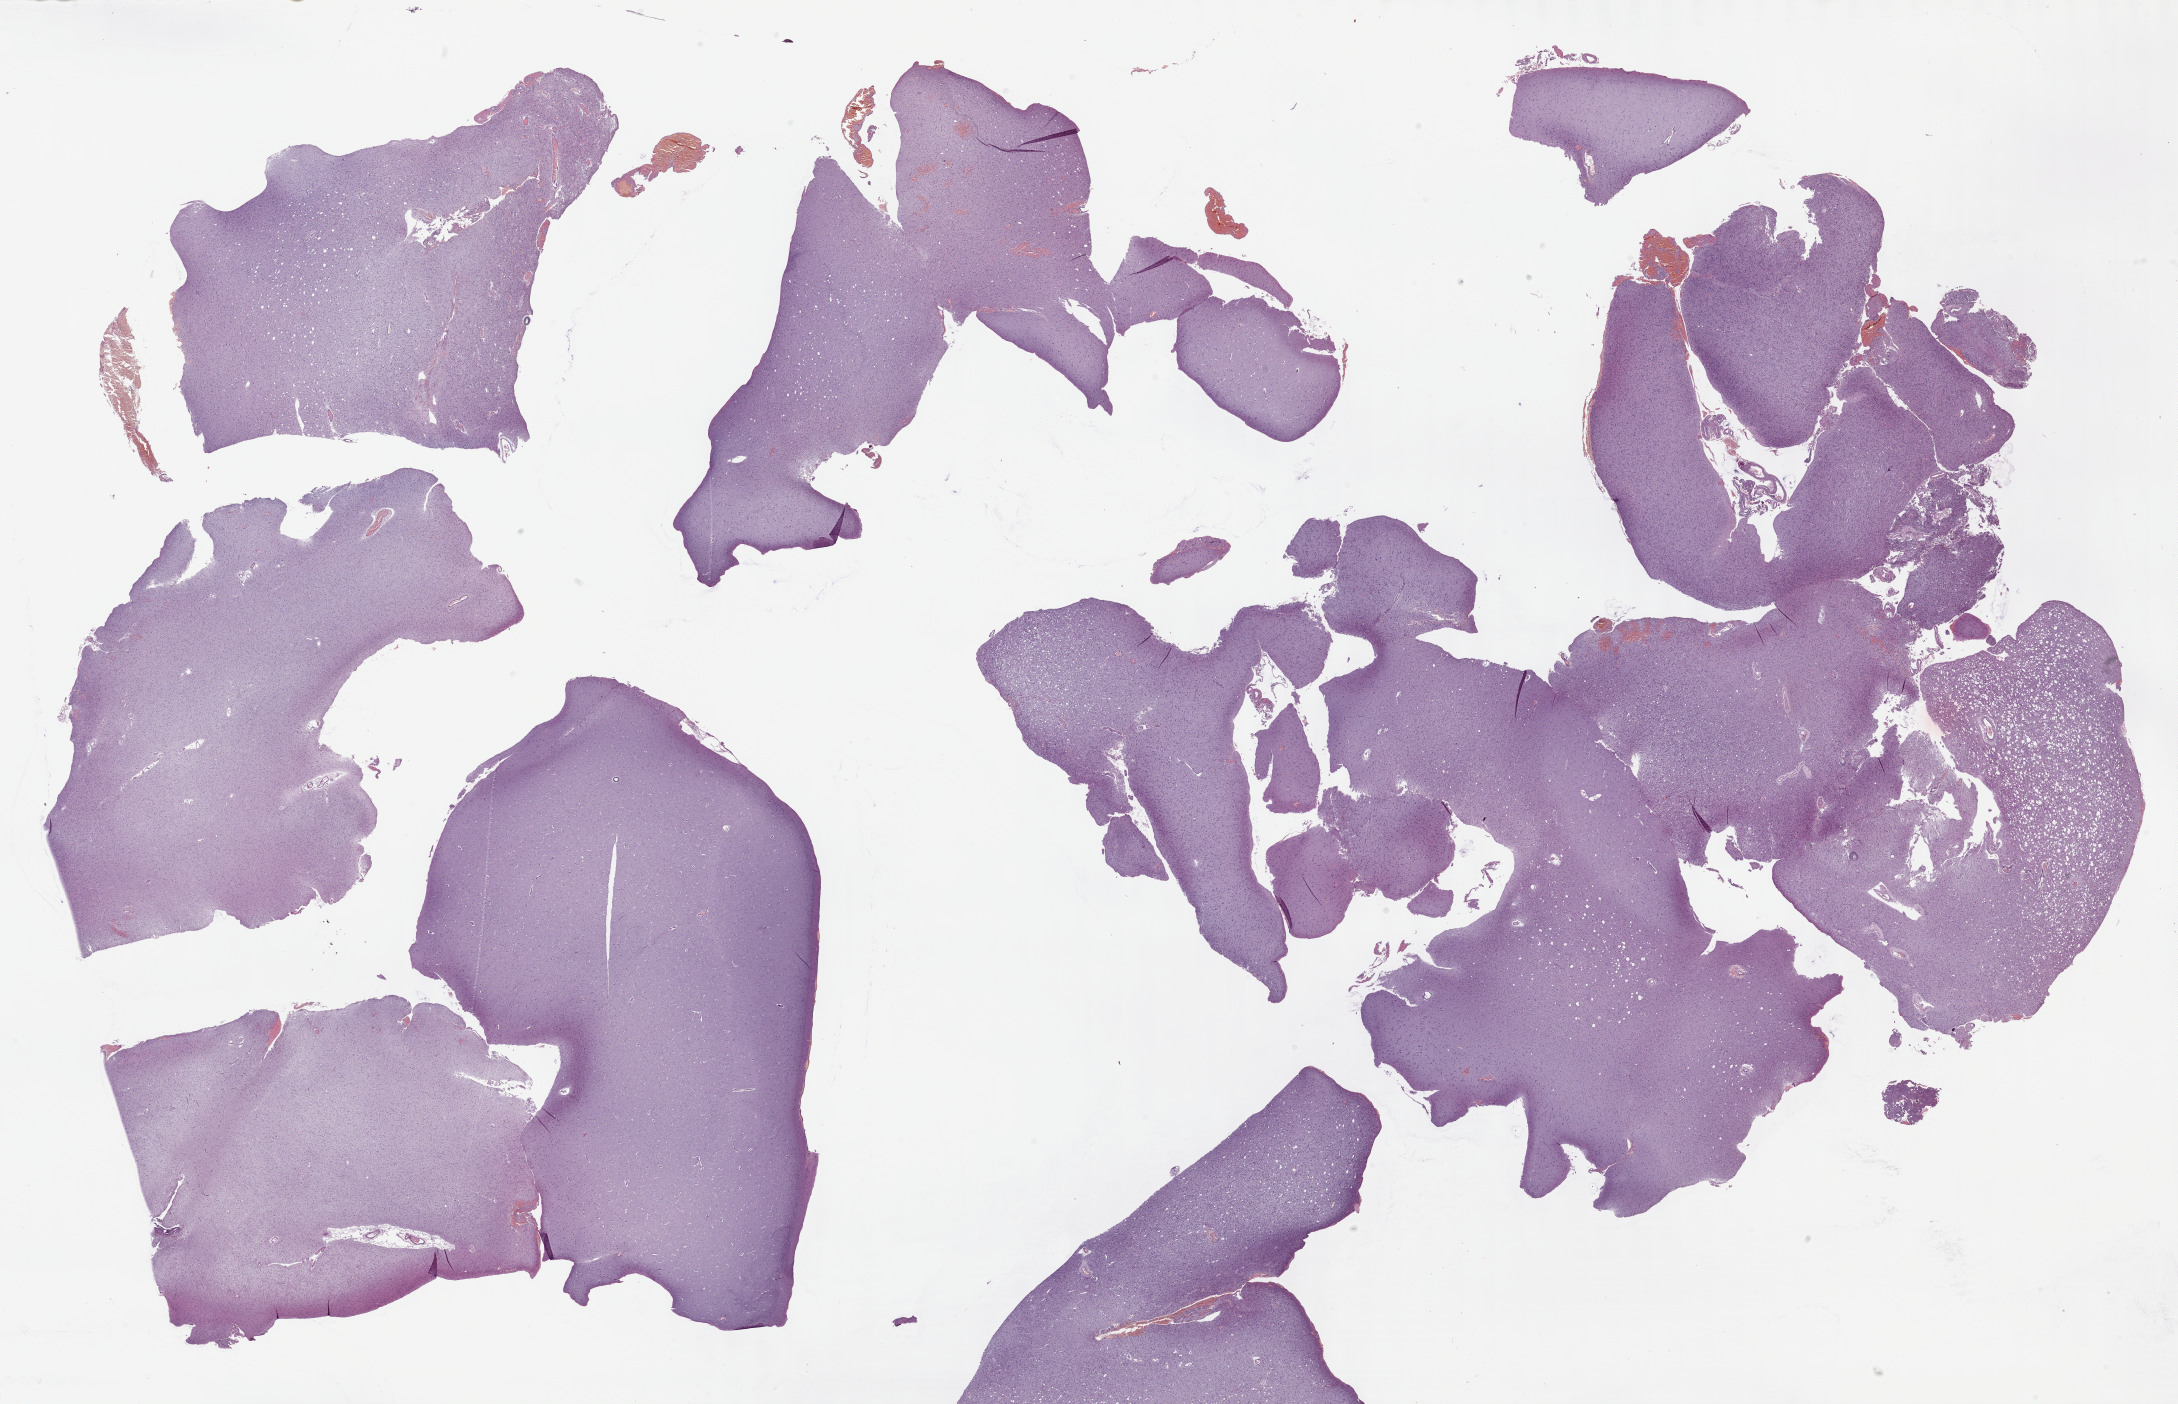
H&E whole-slide image — whole scanned area (about 35.2 x 22.7 mm) shown as a low-resolution overview; formalin-fixed paraffin-embedded (FFPE) diagnostic section; brain, primary tumour sample. Patient: male, age at initial diagnosis 21 years. Histologic grade: G3 (poorly differentiated).
Diagnosis: Astrocytoma, anaplastic (cerebrum). Laterality: left.